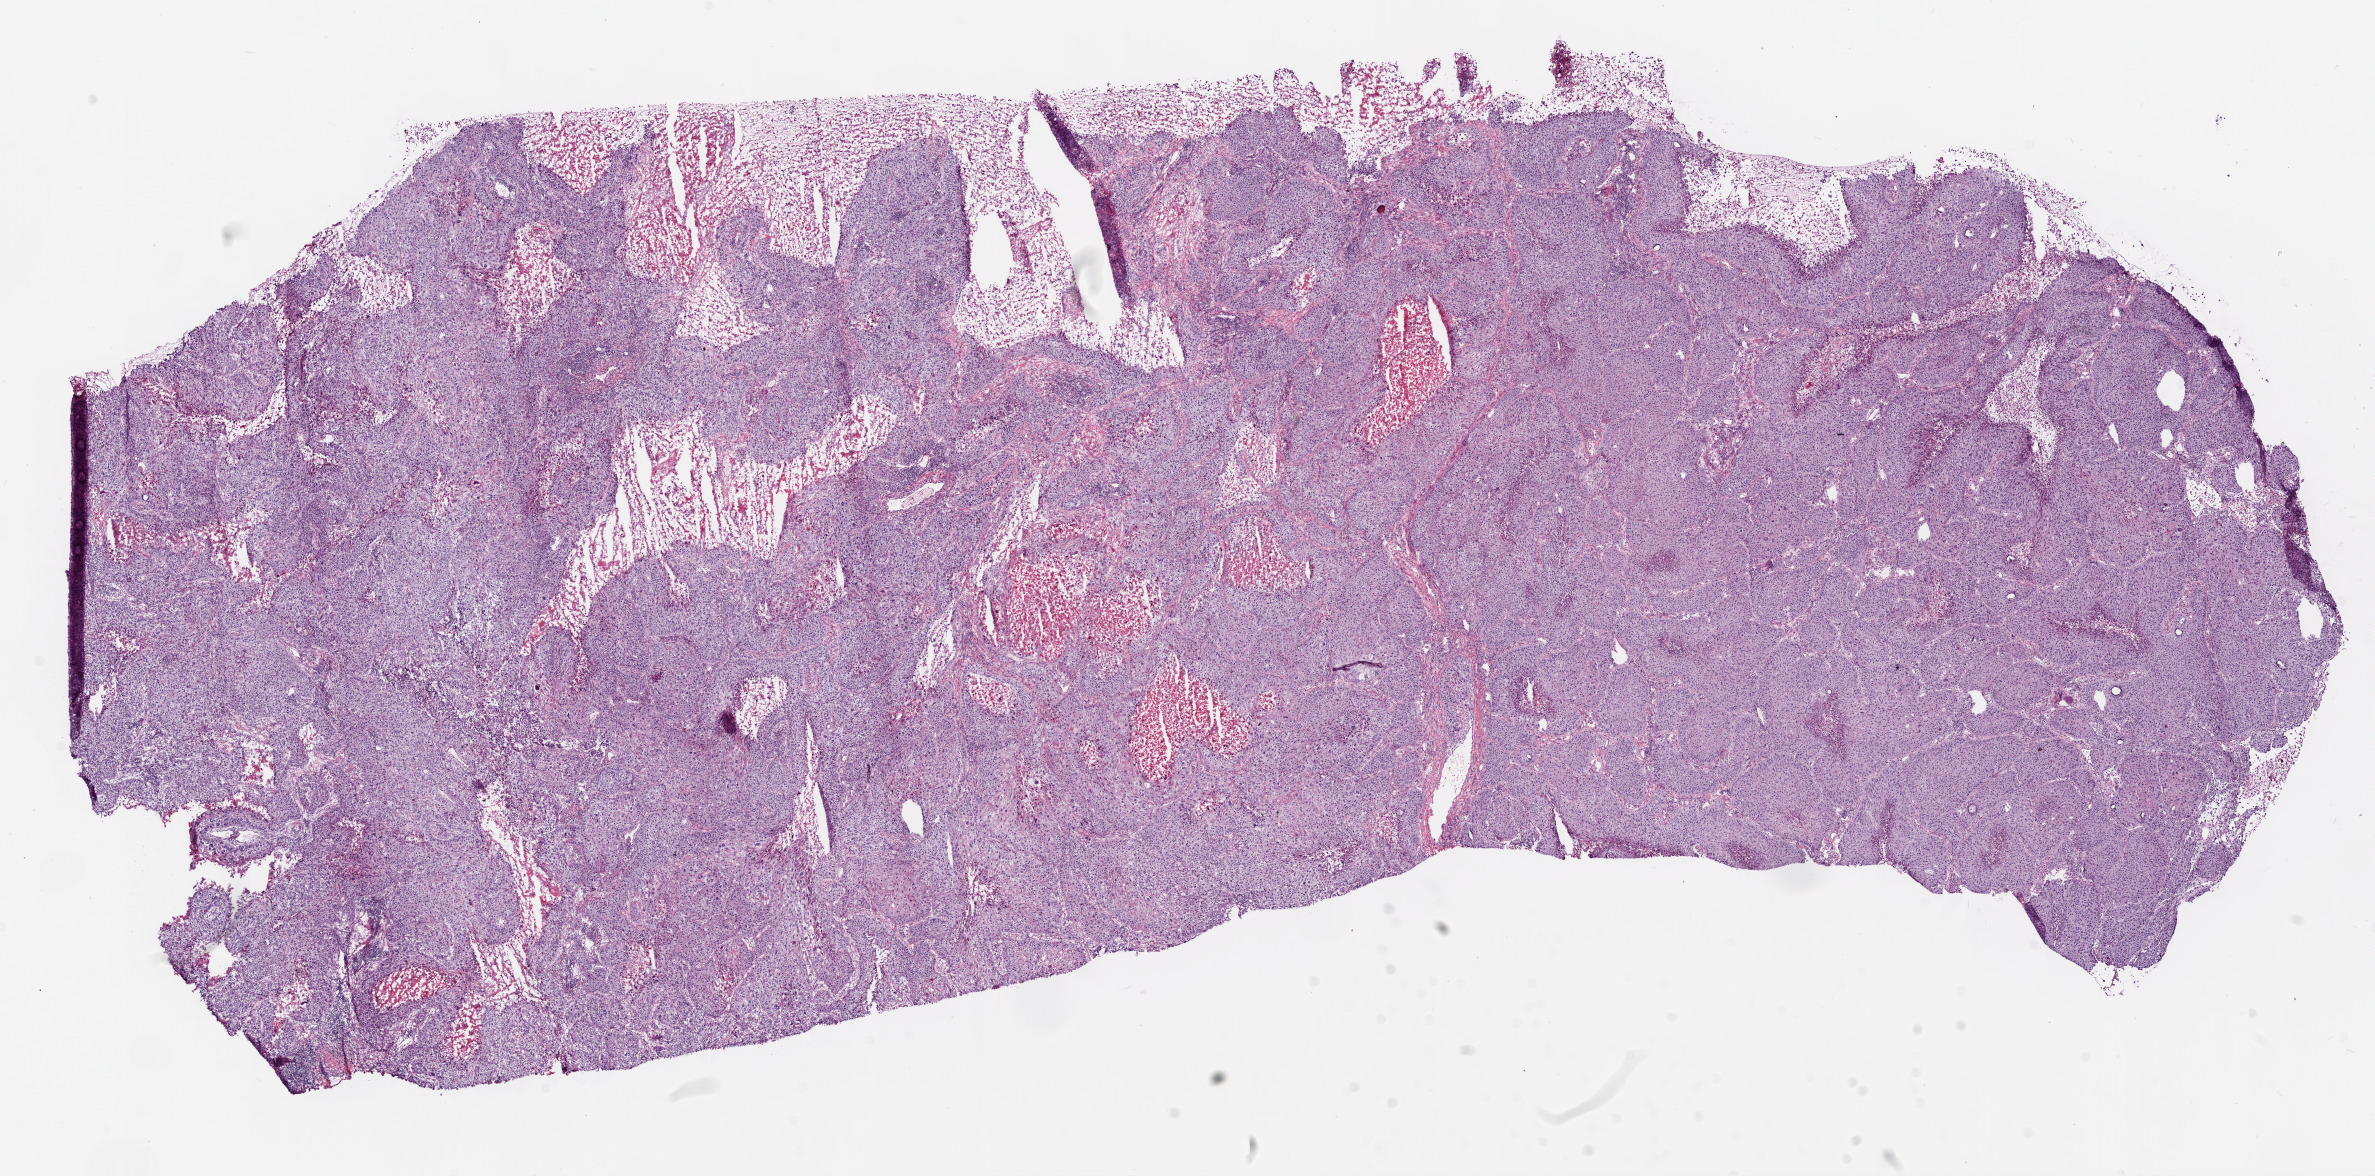
Whole-slide histology image, H&E-stained, whole scanned area (about 19.1 x 9.4 mm, slide scanned at 20x) shown as a low-resolution overview, frozen section from the bottom of the tissue portion, primary tumour sample from the lung. Patient: male, age at initial diagnosis 54 years. Pathologist review of this section (percent, as recorded): tumour cells 75%, tumour nuclei 90%, normal cells 0%, stromal cells 5%, necrosis 20%.
AJCC pathologic stage: IIIA (6th edition). TNM: T2 N2 M0. Histologic diagnosis: Squamous cell carcinoma, NOS (upper lobe, lung).